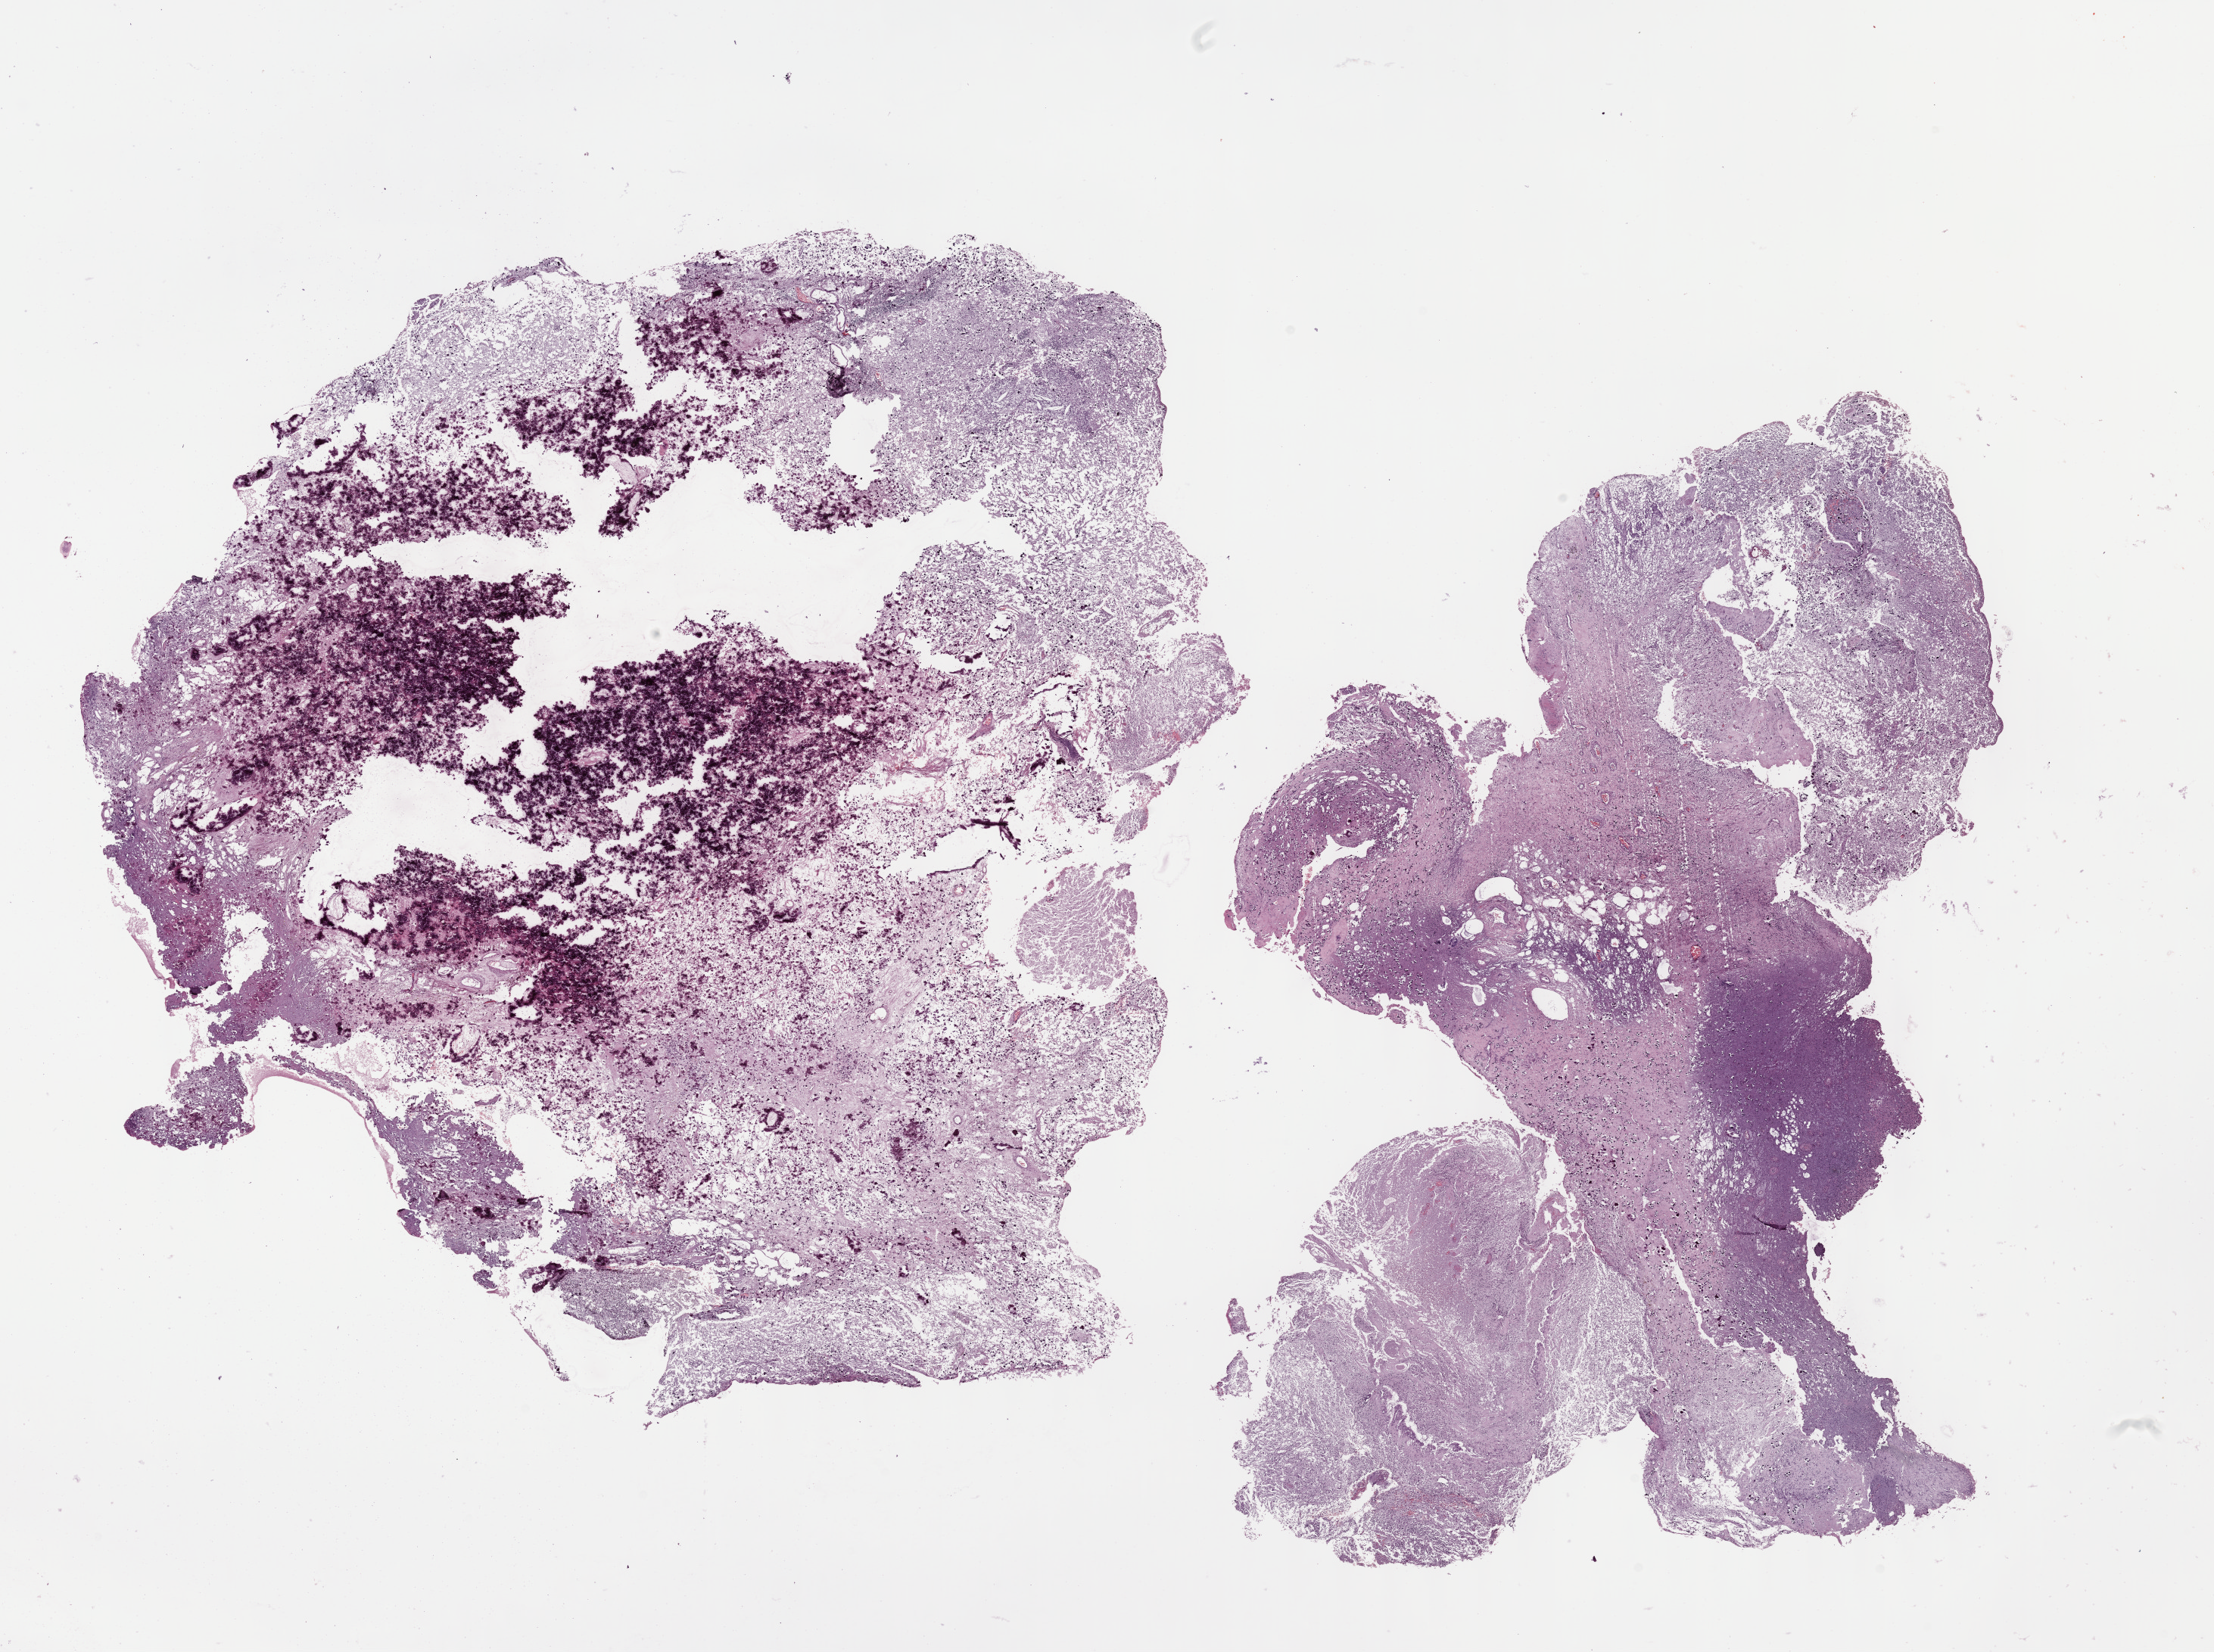
Hematoxylin and eosin (H&E) stained whole-slide image — low-resolution overview of the scanned area, about 23.6 x 17.6 mm (acquisition: 40x scan), FFPE section, brain, primary tumour sample. Female, age 71 years at initial diagnosis. Histologic grade: G3 (poorly differentiated).
Pathologic diagnosis: Oligodendroglioma, anaplastic (cerebrum).